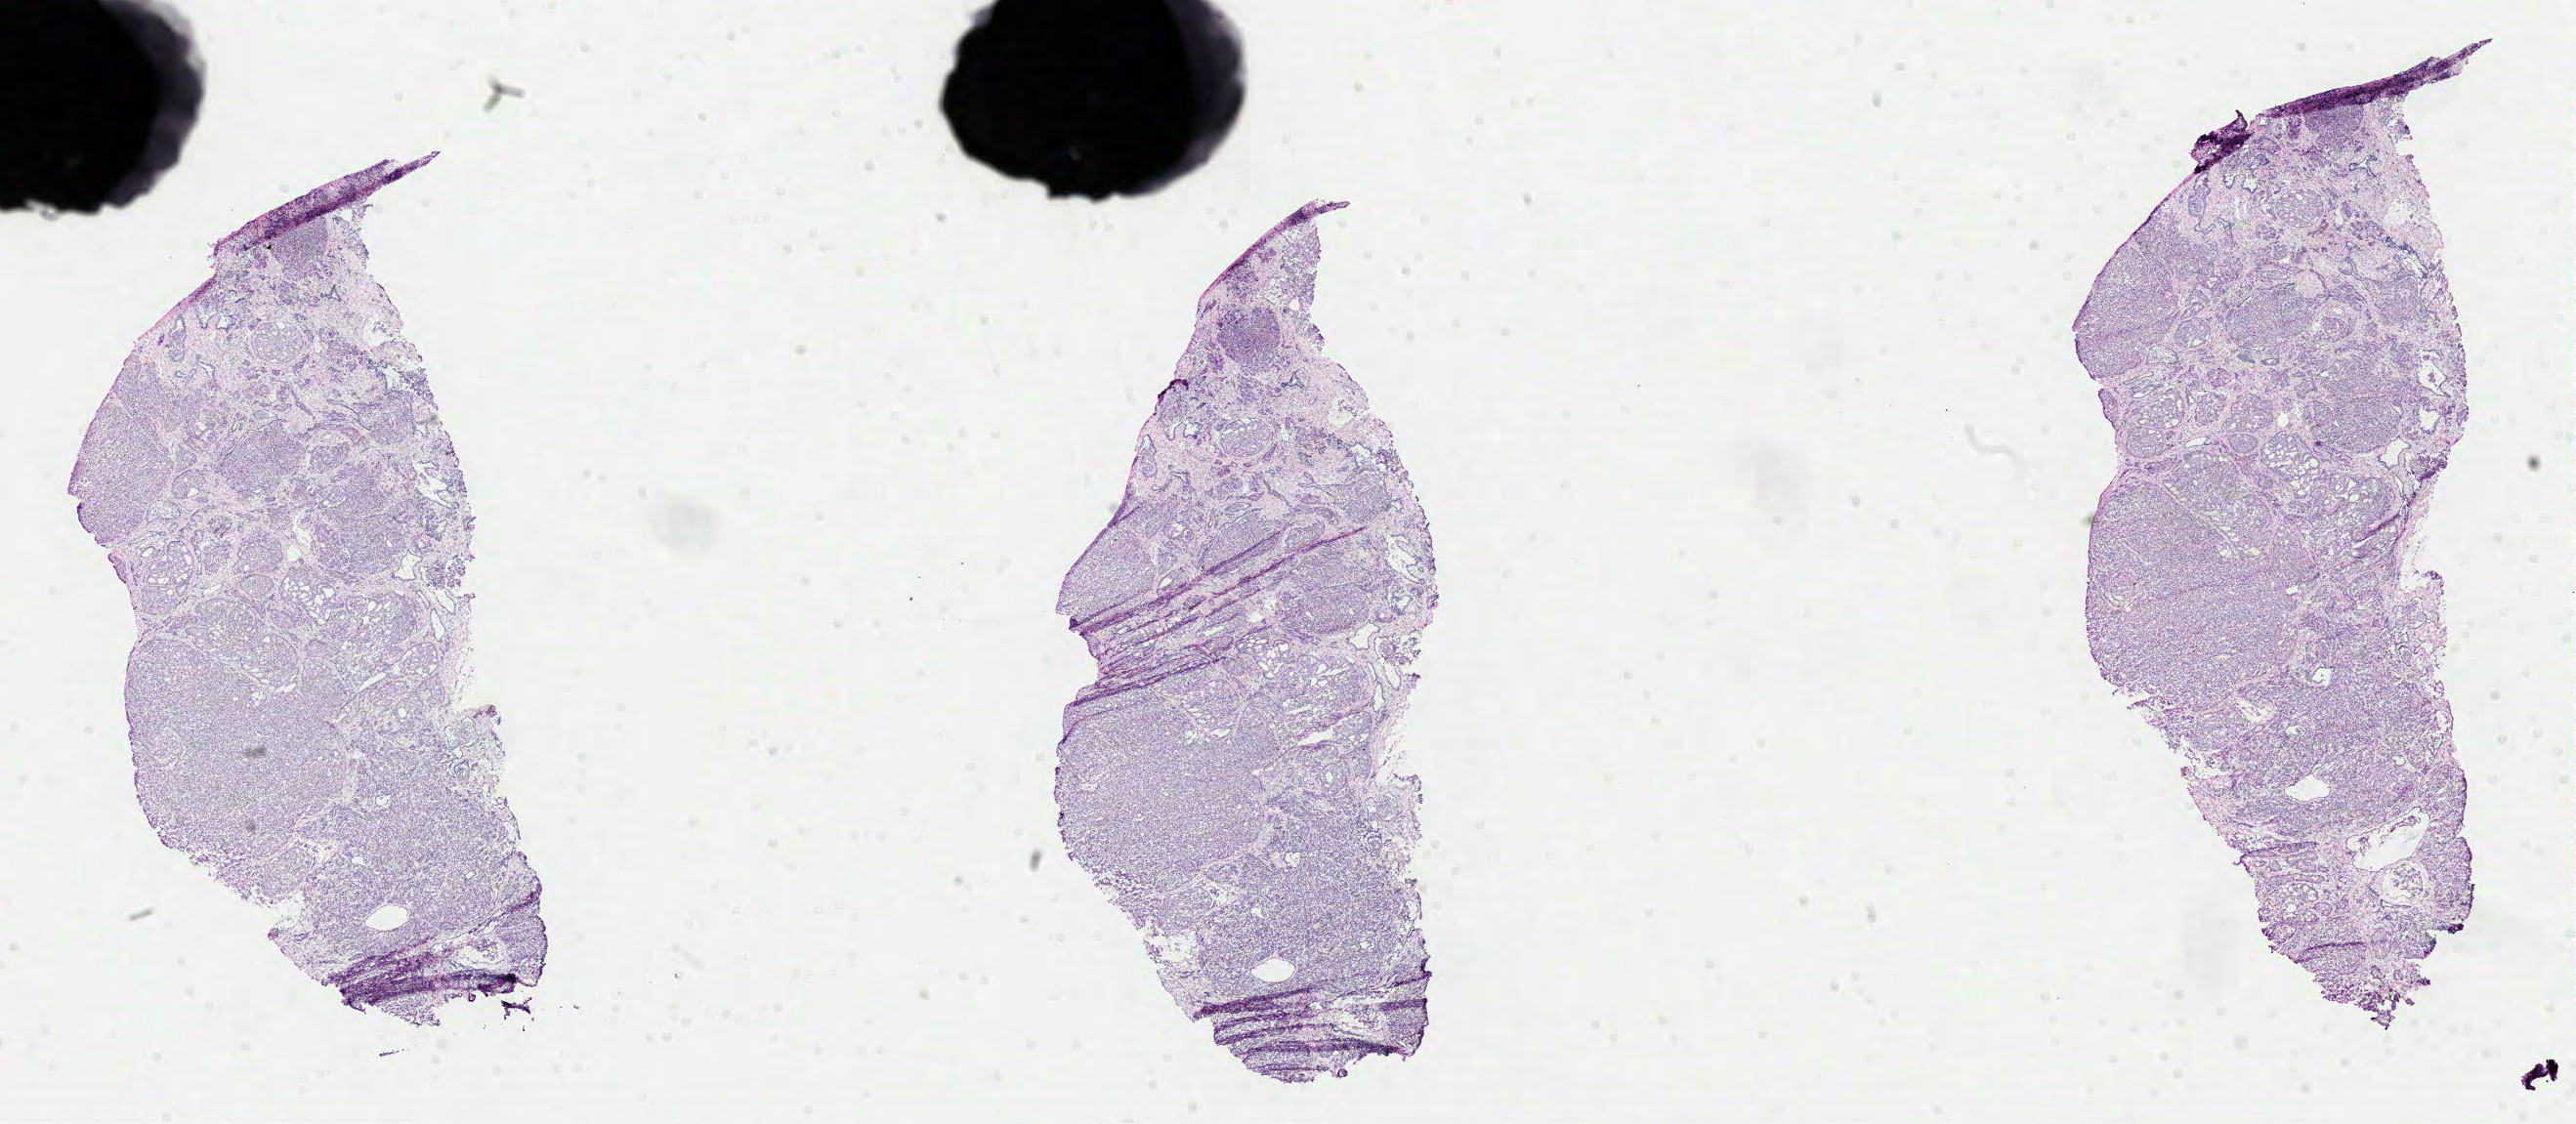
Hematoxylin and eosin (H&E) stained whole-slide image — whole scanned area (about 21.3 x 9.3 mm, acquisition: 40x scan) shown as a low-resolution overview; formalin-fixed paraffin-embedded (FFPE) diagnostic section; sample: primary tumour, prostate. Male patient; age at initial diagnosis 56 years. Gleason score: 9 (4+5).
• lymph nodes positive (case pathology): 1 of 5 examined
• pathologic diagnosis: Acinar cell carcinoma (prostate gland)
• laterality: bilateral